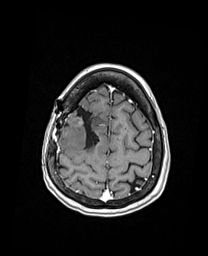
Brain MRI from a brain-tumour surgery series, one axial slice. Slice 41 of 192 in the series (ordered by position). T1-weighted post-contrast. 1 mm slice thickness. 208 × 256 image matrix, field of view 208 × 256 mm. Case-level facts recorded for this patient, not image findings: histopathology: Oligodendroglioma; WHO grade: 3; IDH mutation: yes.
Structures marked on this image (manually delineated by an expert):
- previous resection cavity: box from (x=72, y=109) to (x=99, y=148) px